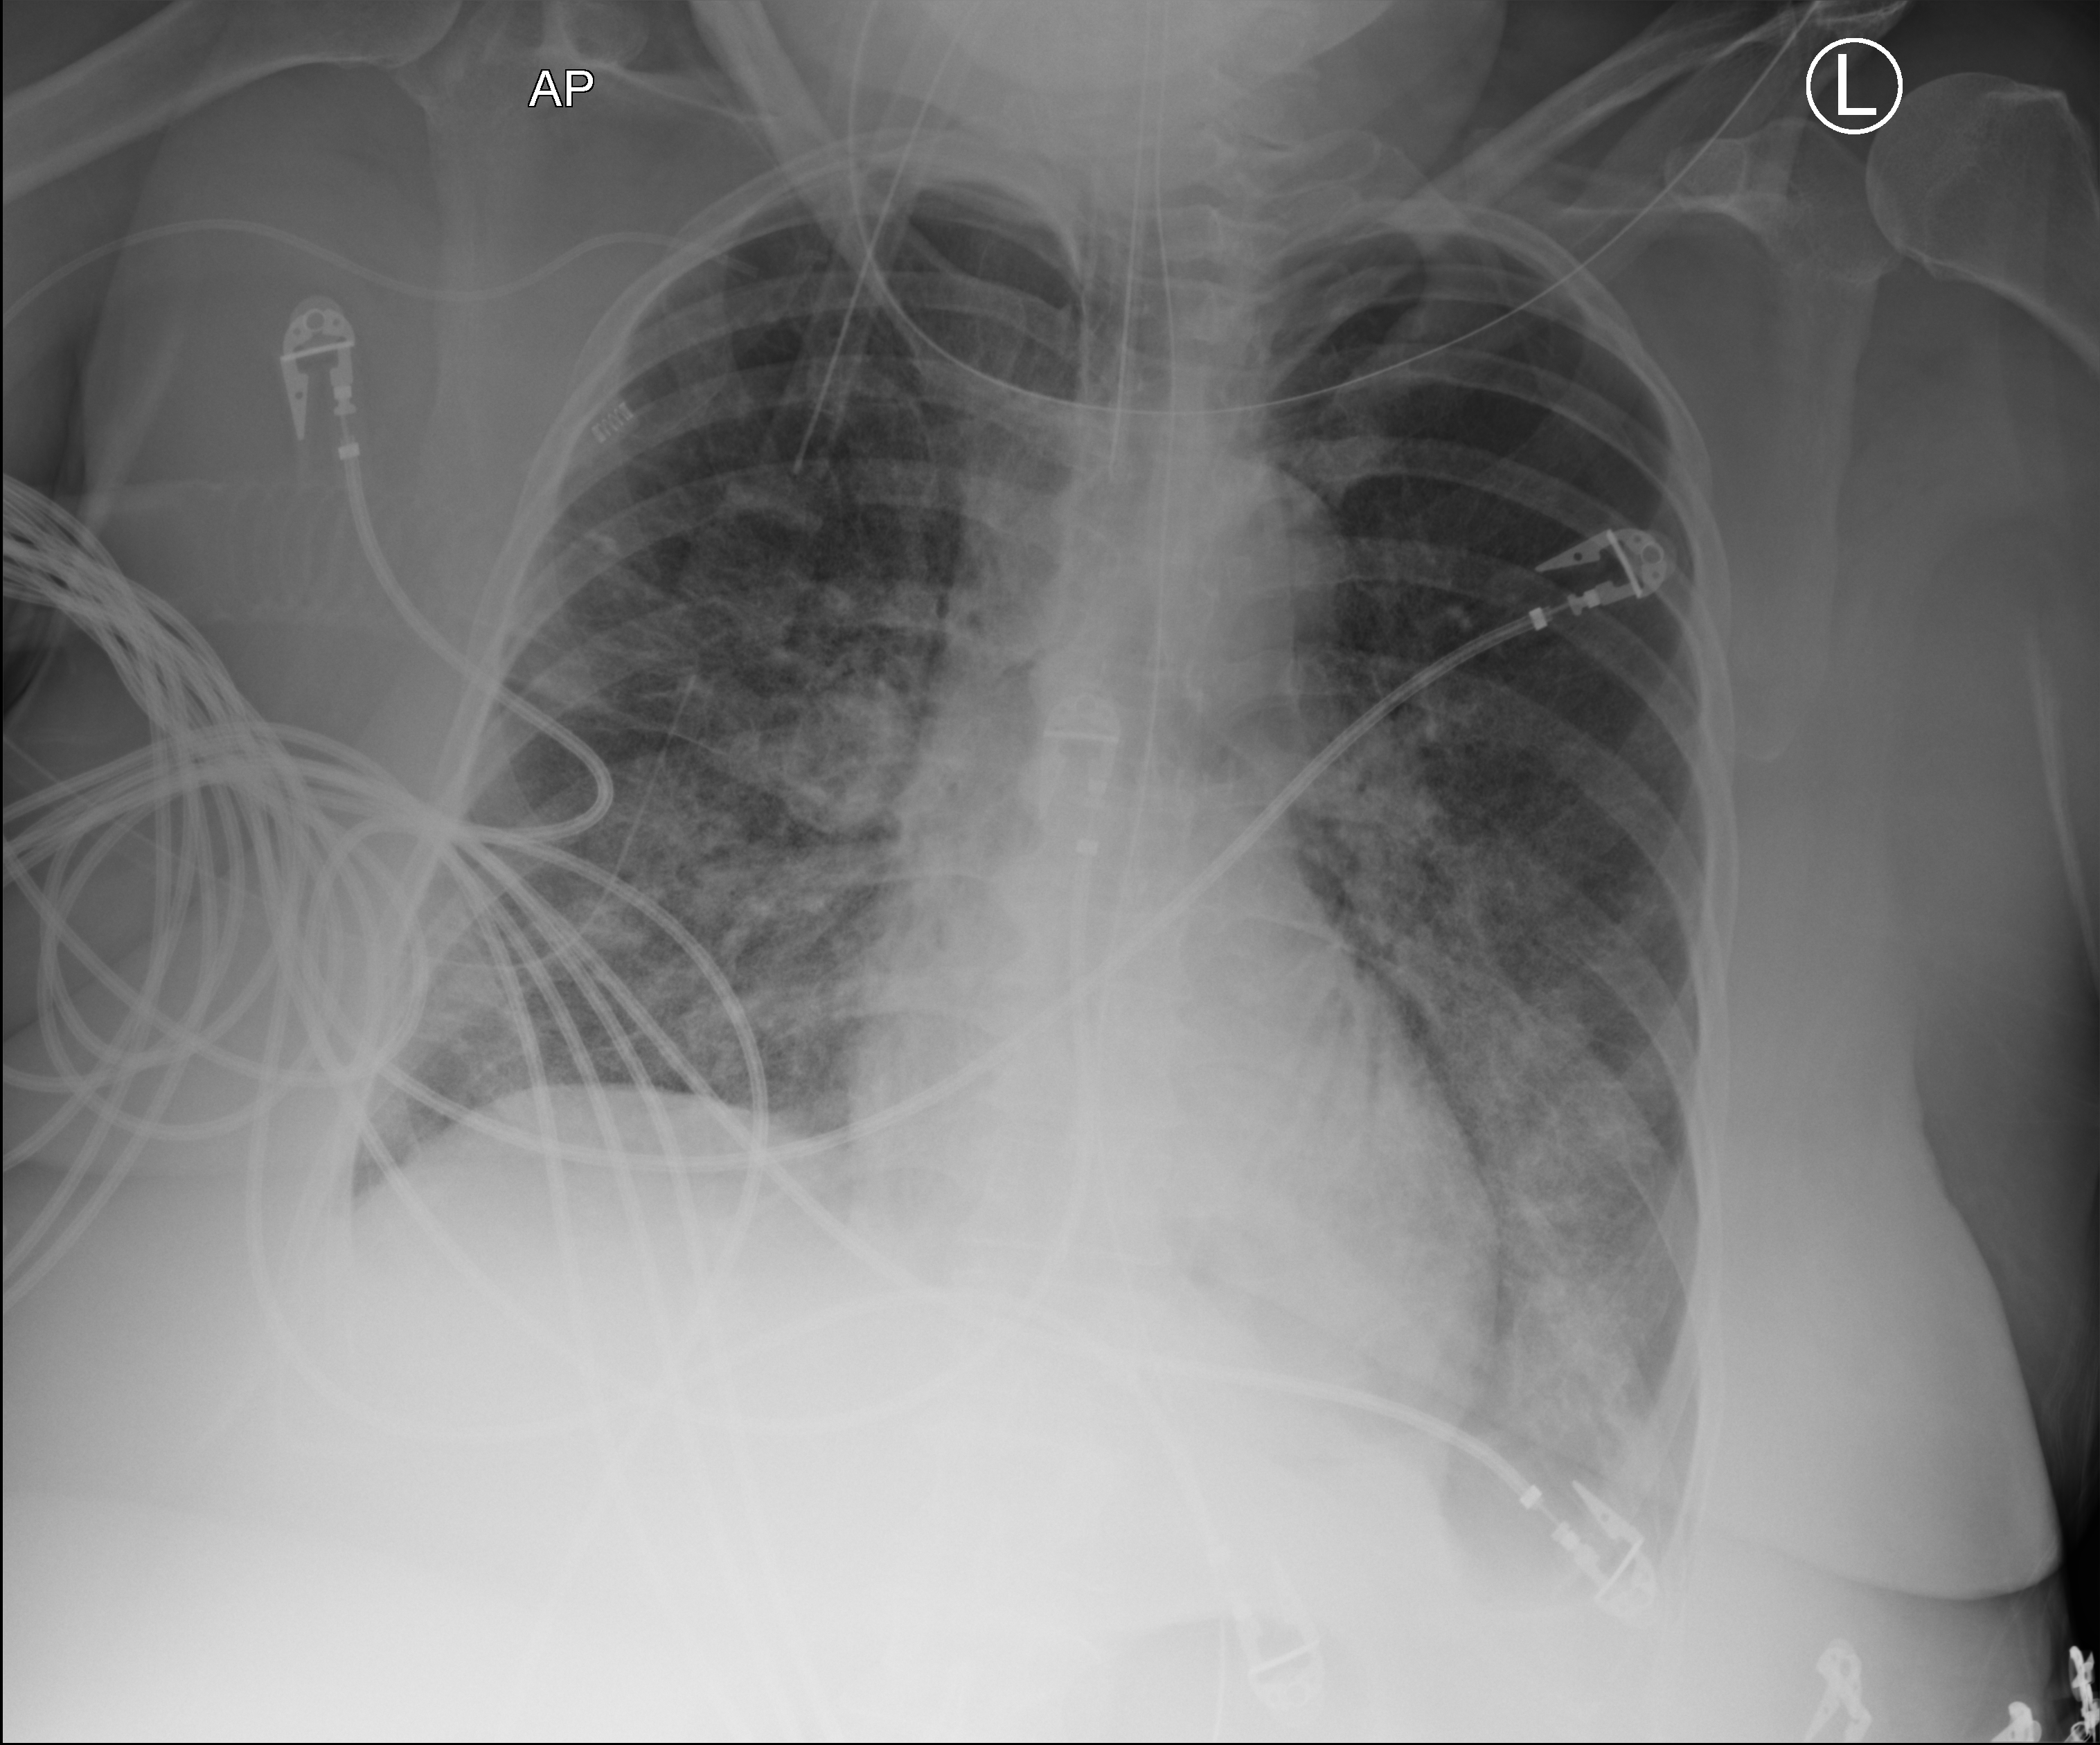
Portable chest radiograph. Female patient hospitalised with COVID-19, age 60–74 years.
Admission-level facts for this patient (not findings on this image; timing relative to this image not recorded): admitted to intensive care during this hospital stay: yes.